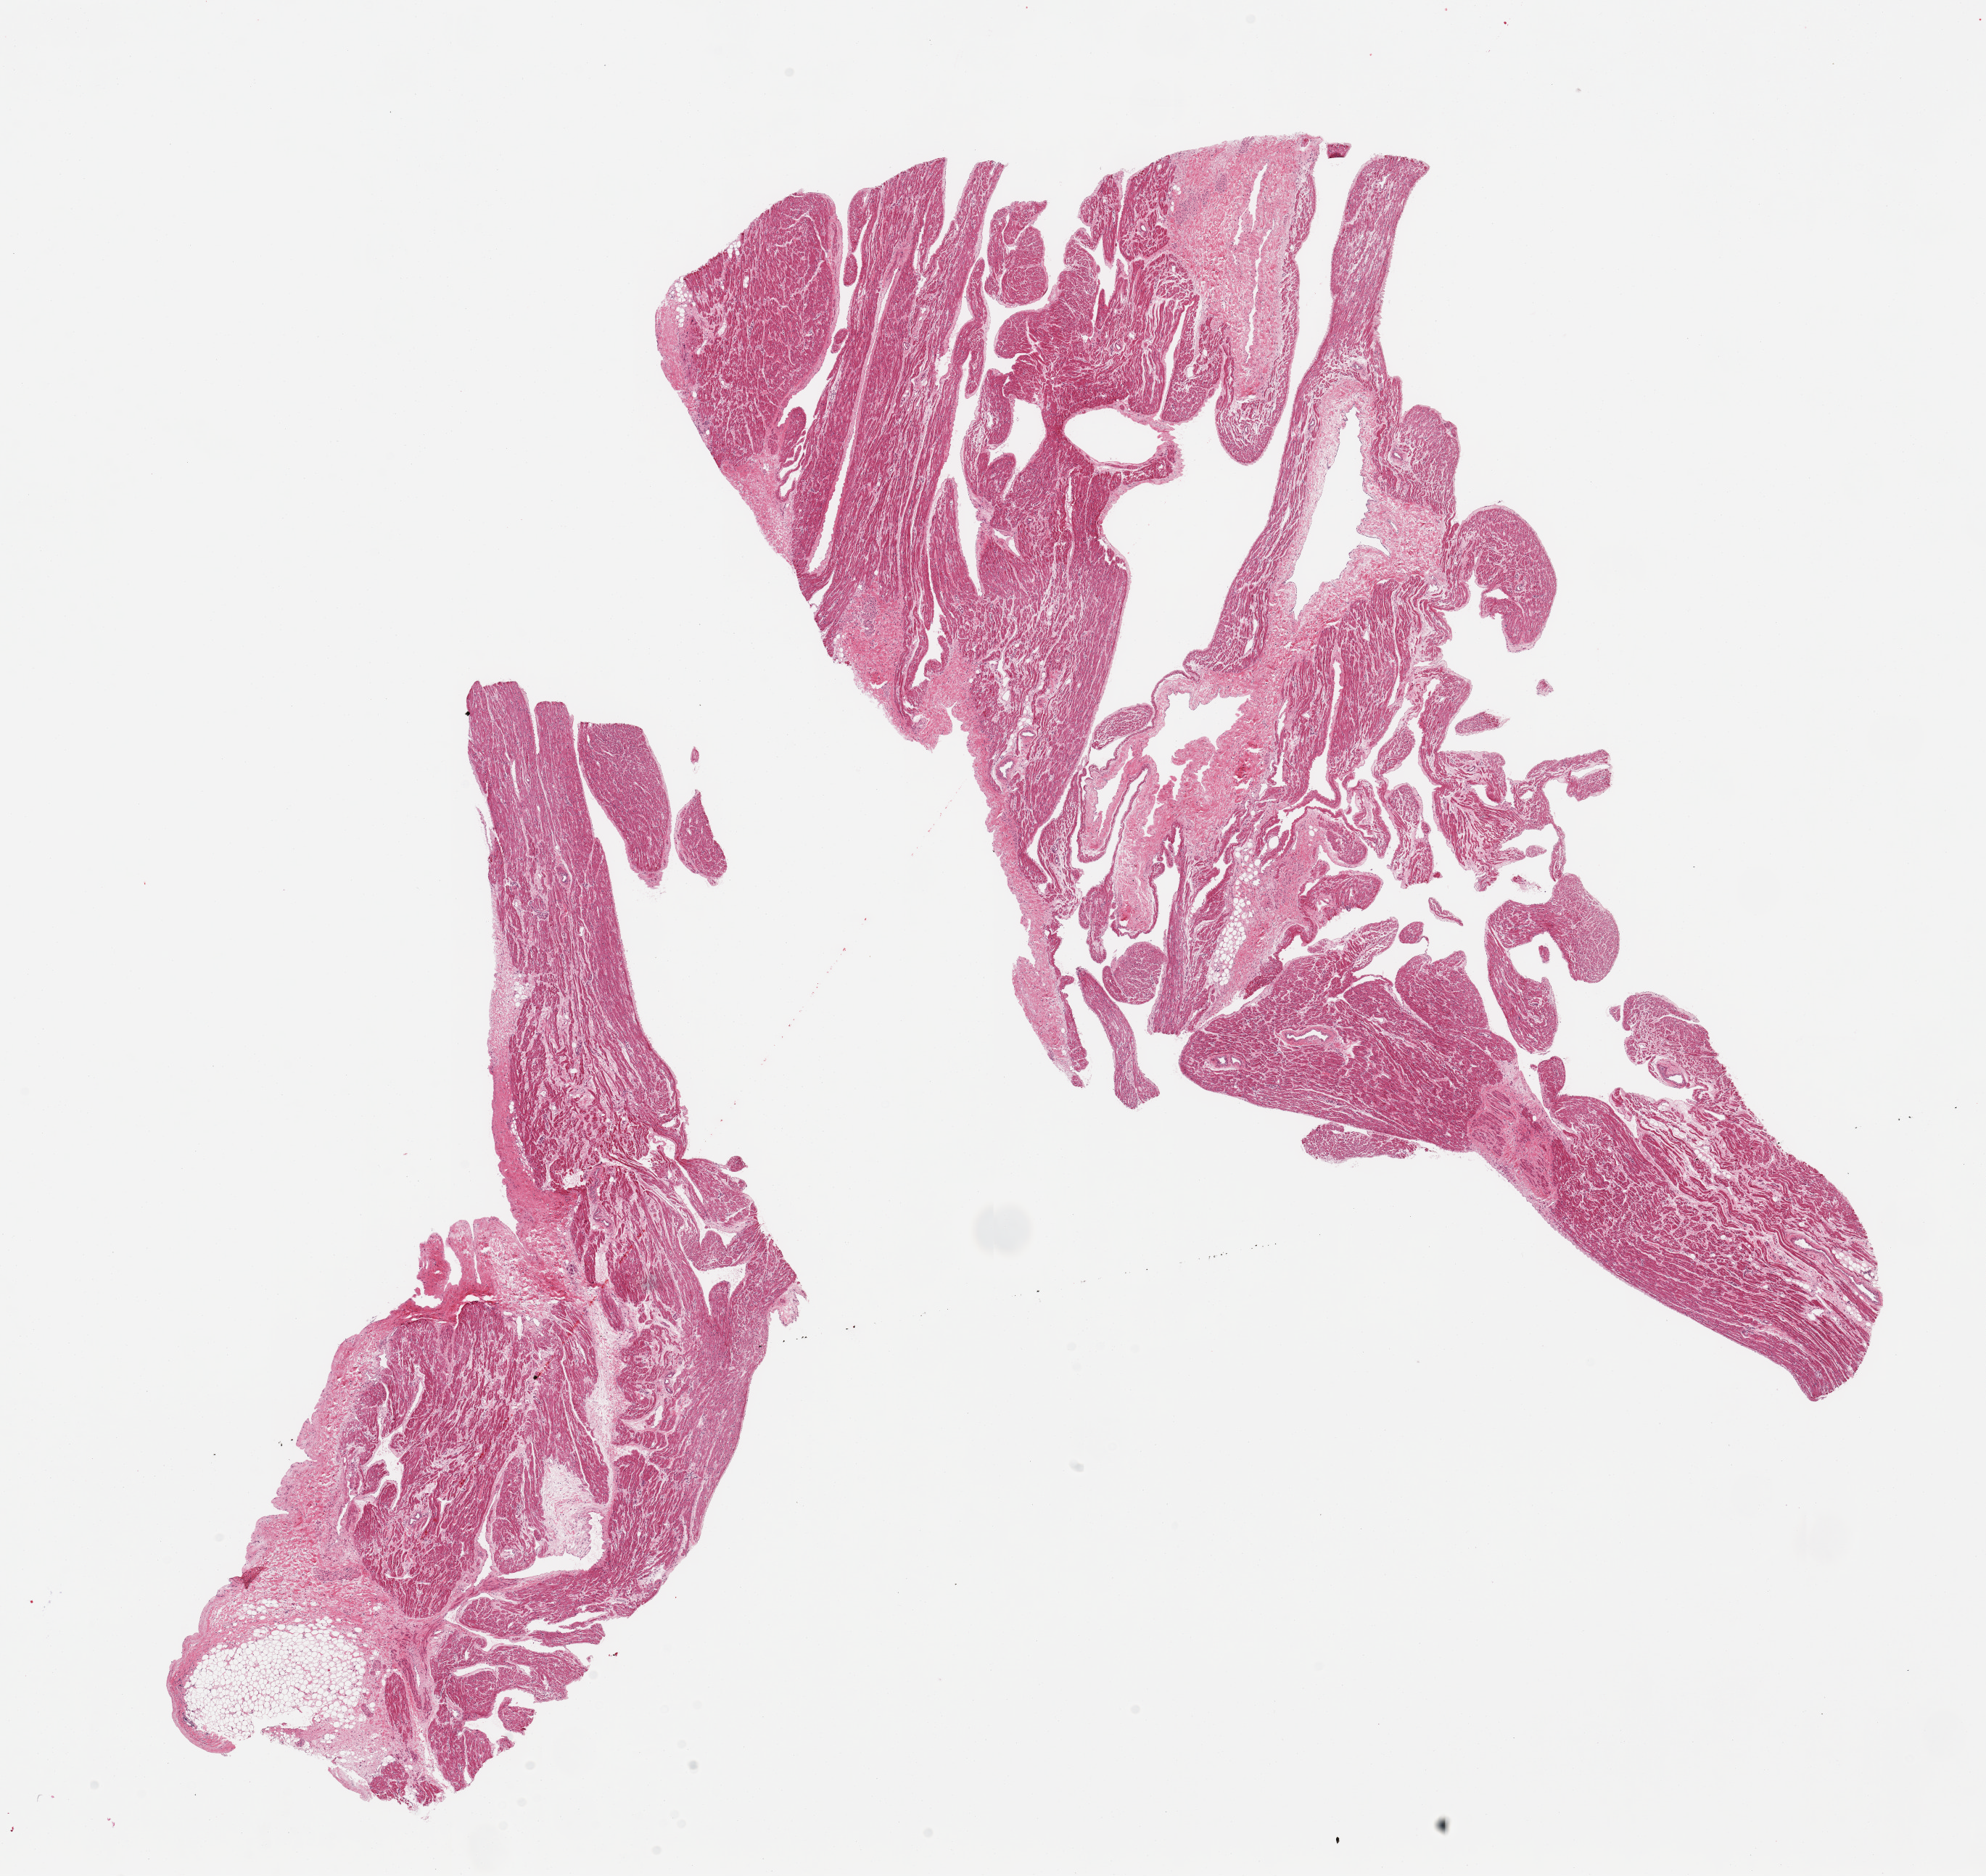
Digitized H&E-stained section, shown as a low-resolution overview of the whole scanned area (about 21.7 x 20.5 mm, from a 20x scan). PAXgene-fixed paraffin-embedded (PFPE) section. Sampled site (target tissue): auricular appendage. Tissue donor sample.
• review note (as recorded): 2 pieces; one piece is ~20% fat/fibrous